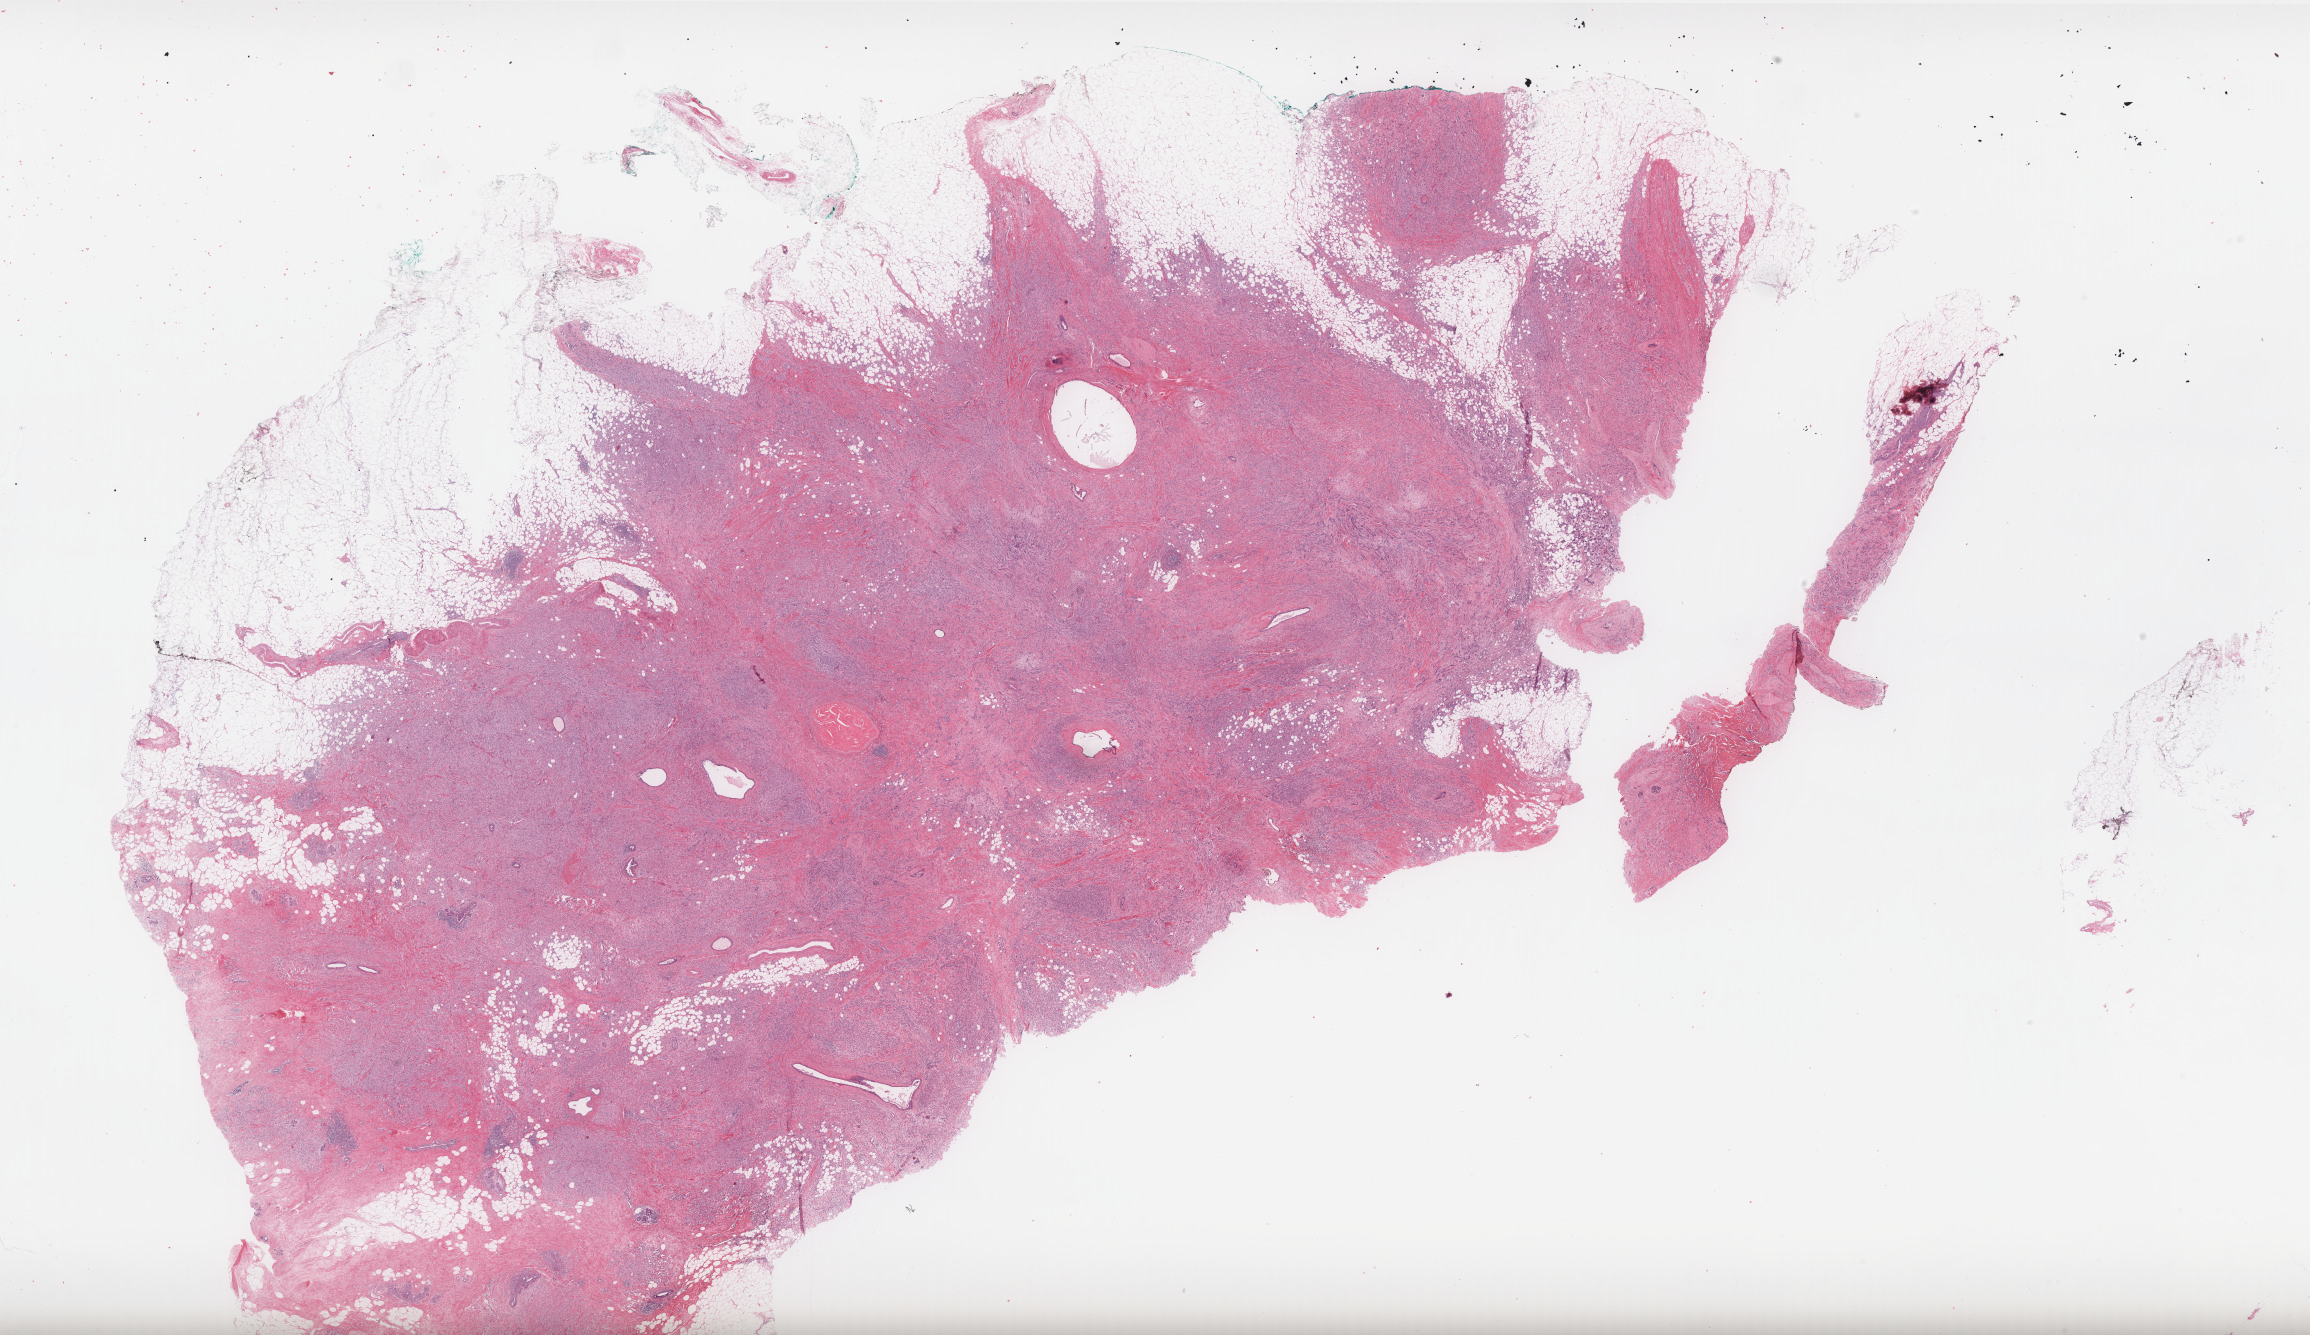
H&E-stained whole-slide image — shown as a low-resolution overview of the whole scanned area (about 37.0 x 21.4 mm, slide scanned at 40x). Formalin-fixed paraffin-embedded (FFPE) diagnostic section. Sample: primary tumour, breast. Female, age 63 years at initial diagnosis.
* TNM: T3 N0 (i+) M0
* AJCC pathologic stage: IIB
* diagnosis: Lobular carcinoma, NOS